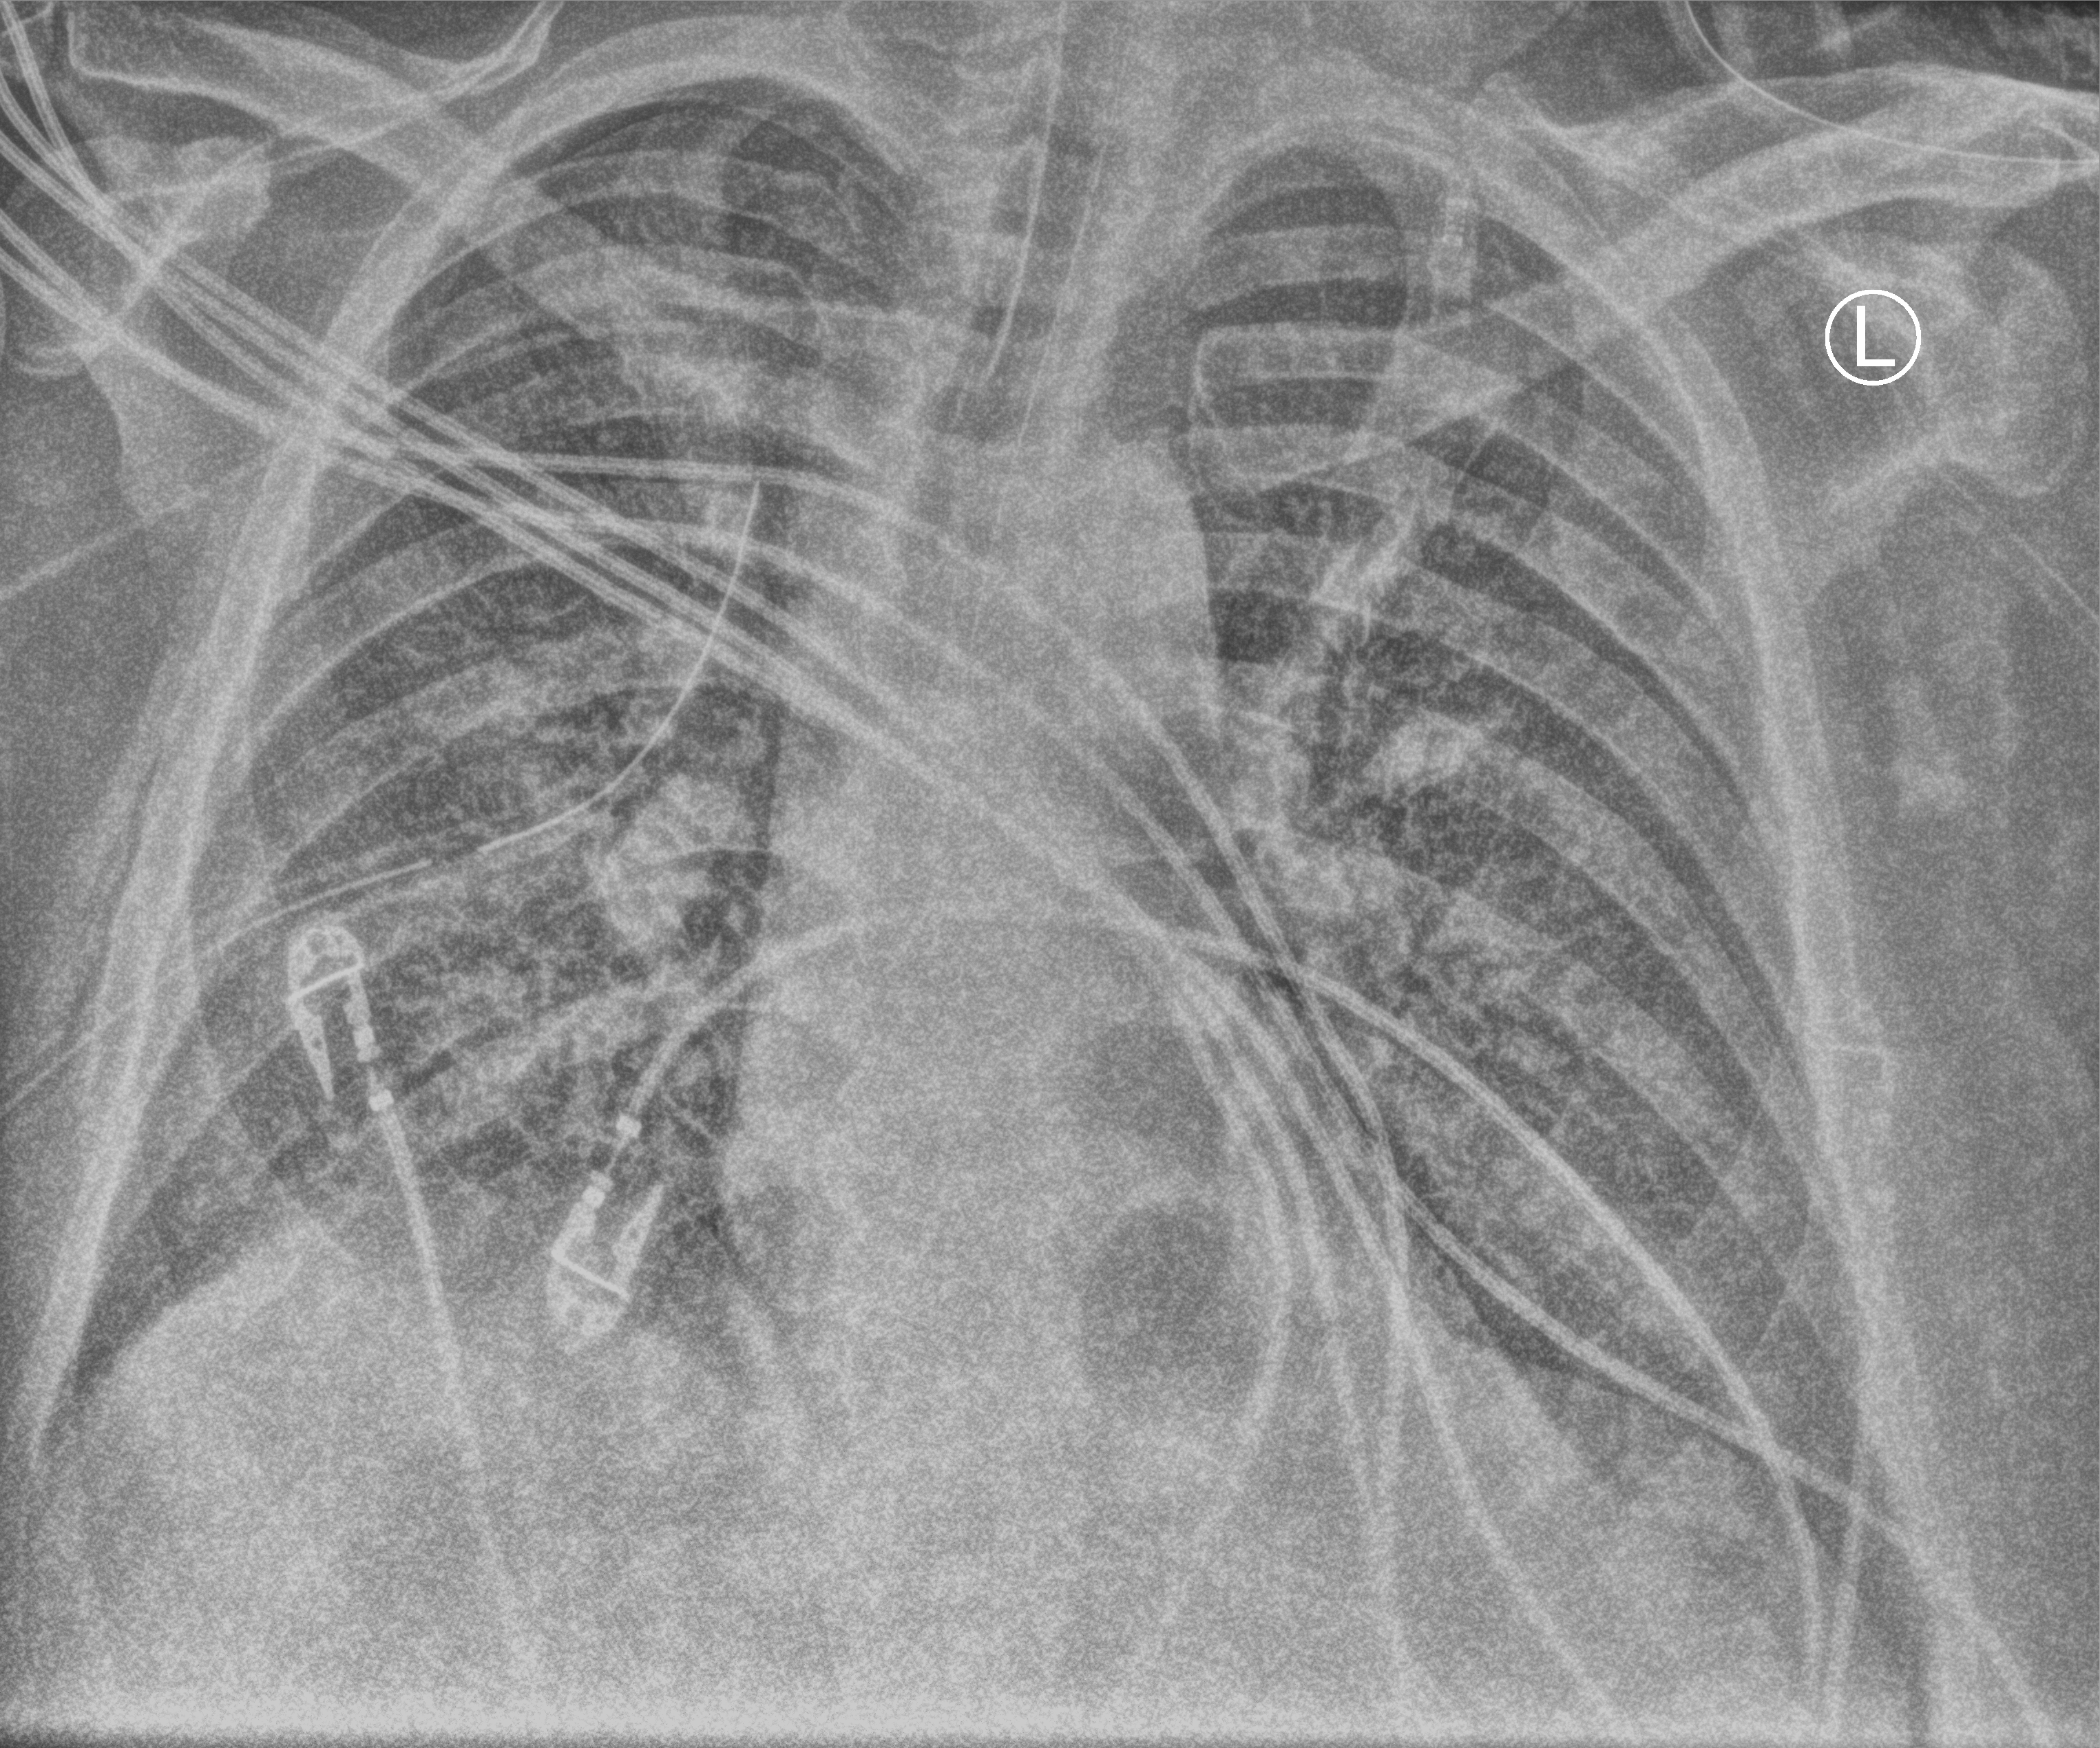
Portable chest radiograph. Adult patient hospitalised with COVID-19, age 18–59 years.
Hospital-stay facts (about this admission, not read from this image; timing relative to this image not recorded):
- mechanically ventilated during this hospital stay: yes
- other chronic lung disease (admission record): no
- admitted to intensive care during this hospital stay: yes